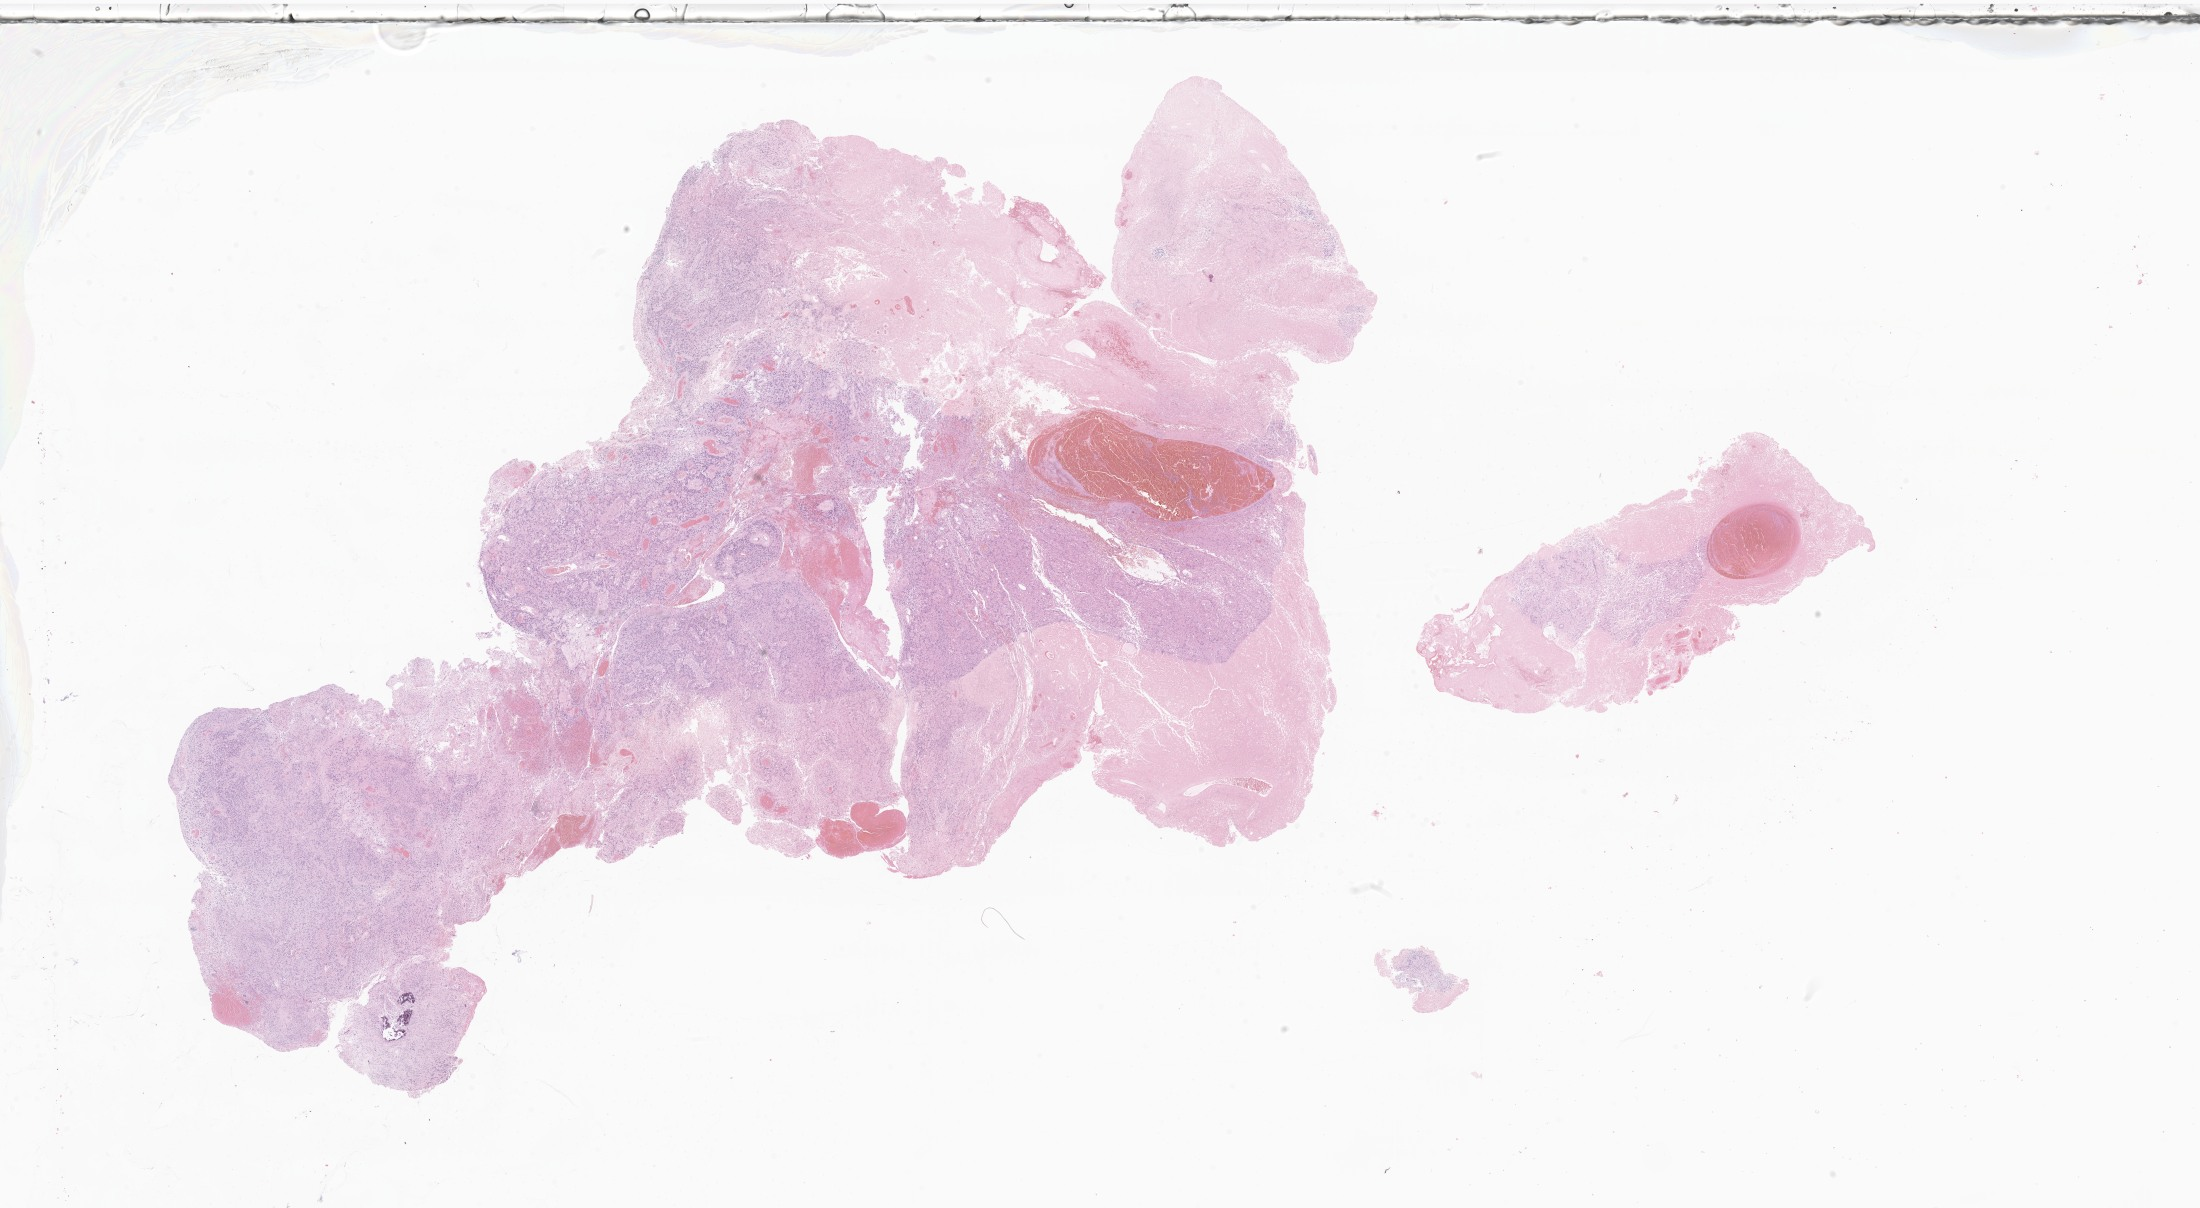
Digitized hematoxylin and eosin (H&E)-stained section of tumor tissue from the brain — a low-resolution overview of the entire scanned area, about 37.1 x 20.4 mm. Formalin-fixed, paraffin-embedded (FFPE) tissue. Patient: female, age 120 months (10 years).
Recorded diagnosis: Ependymoma, NOS.